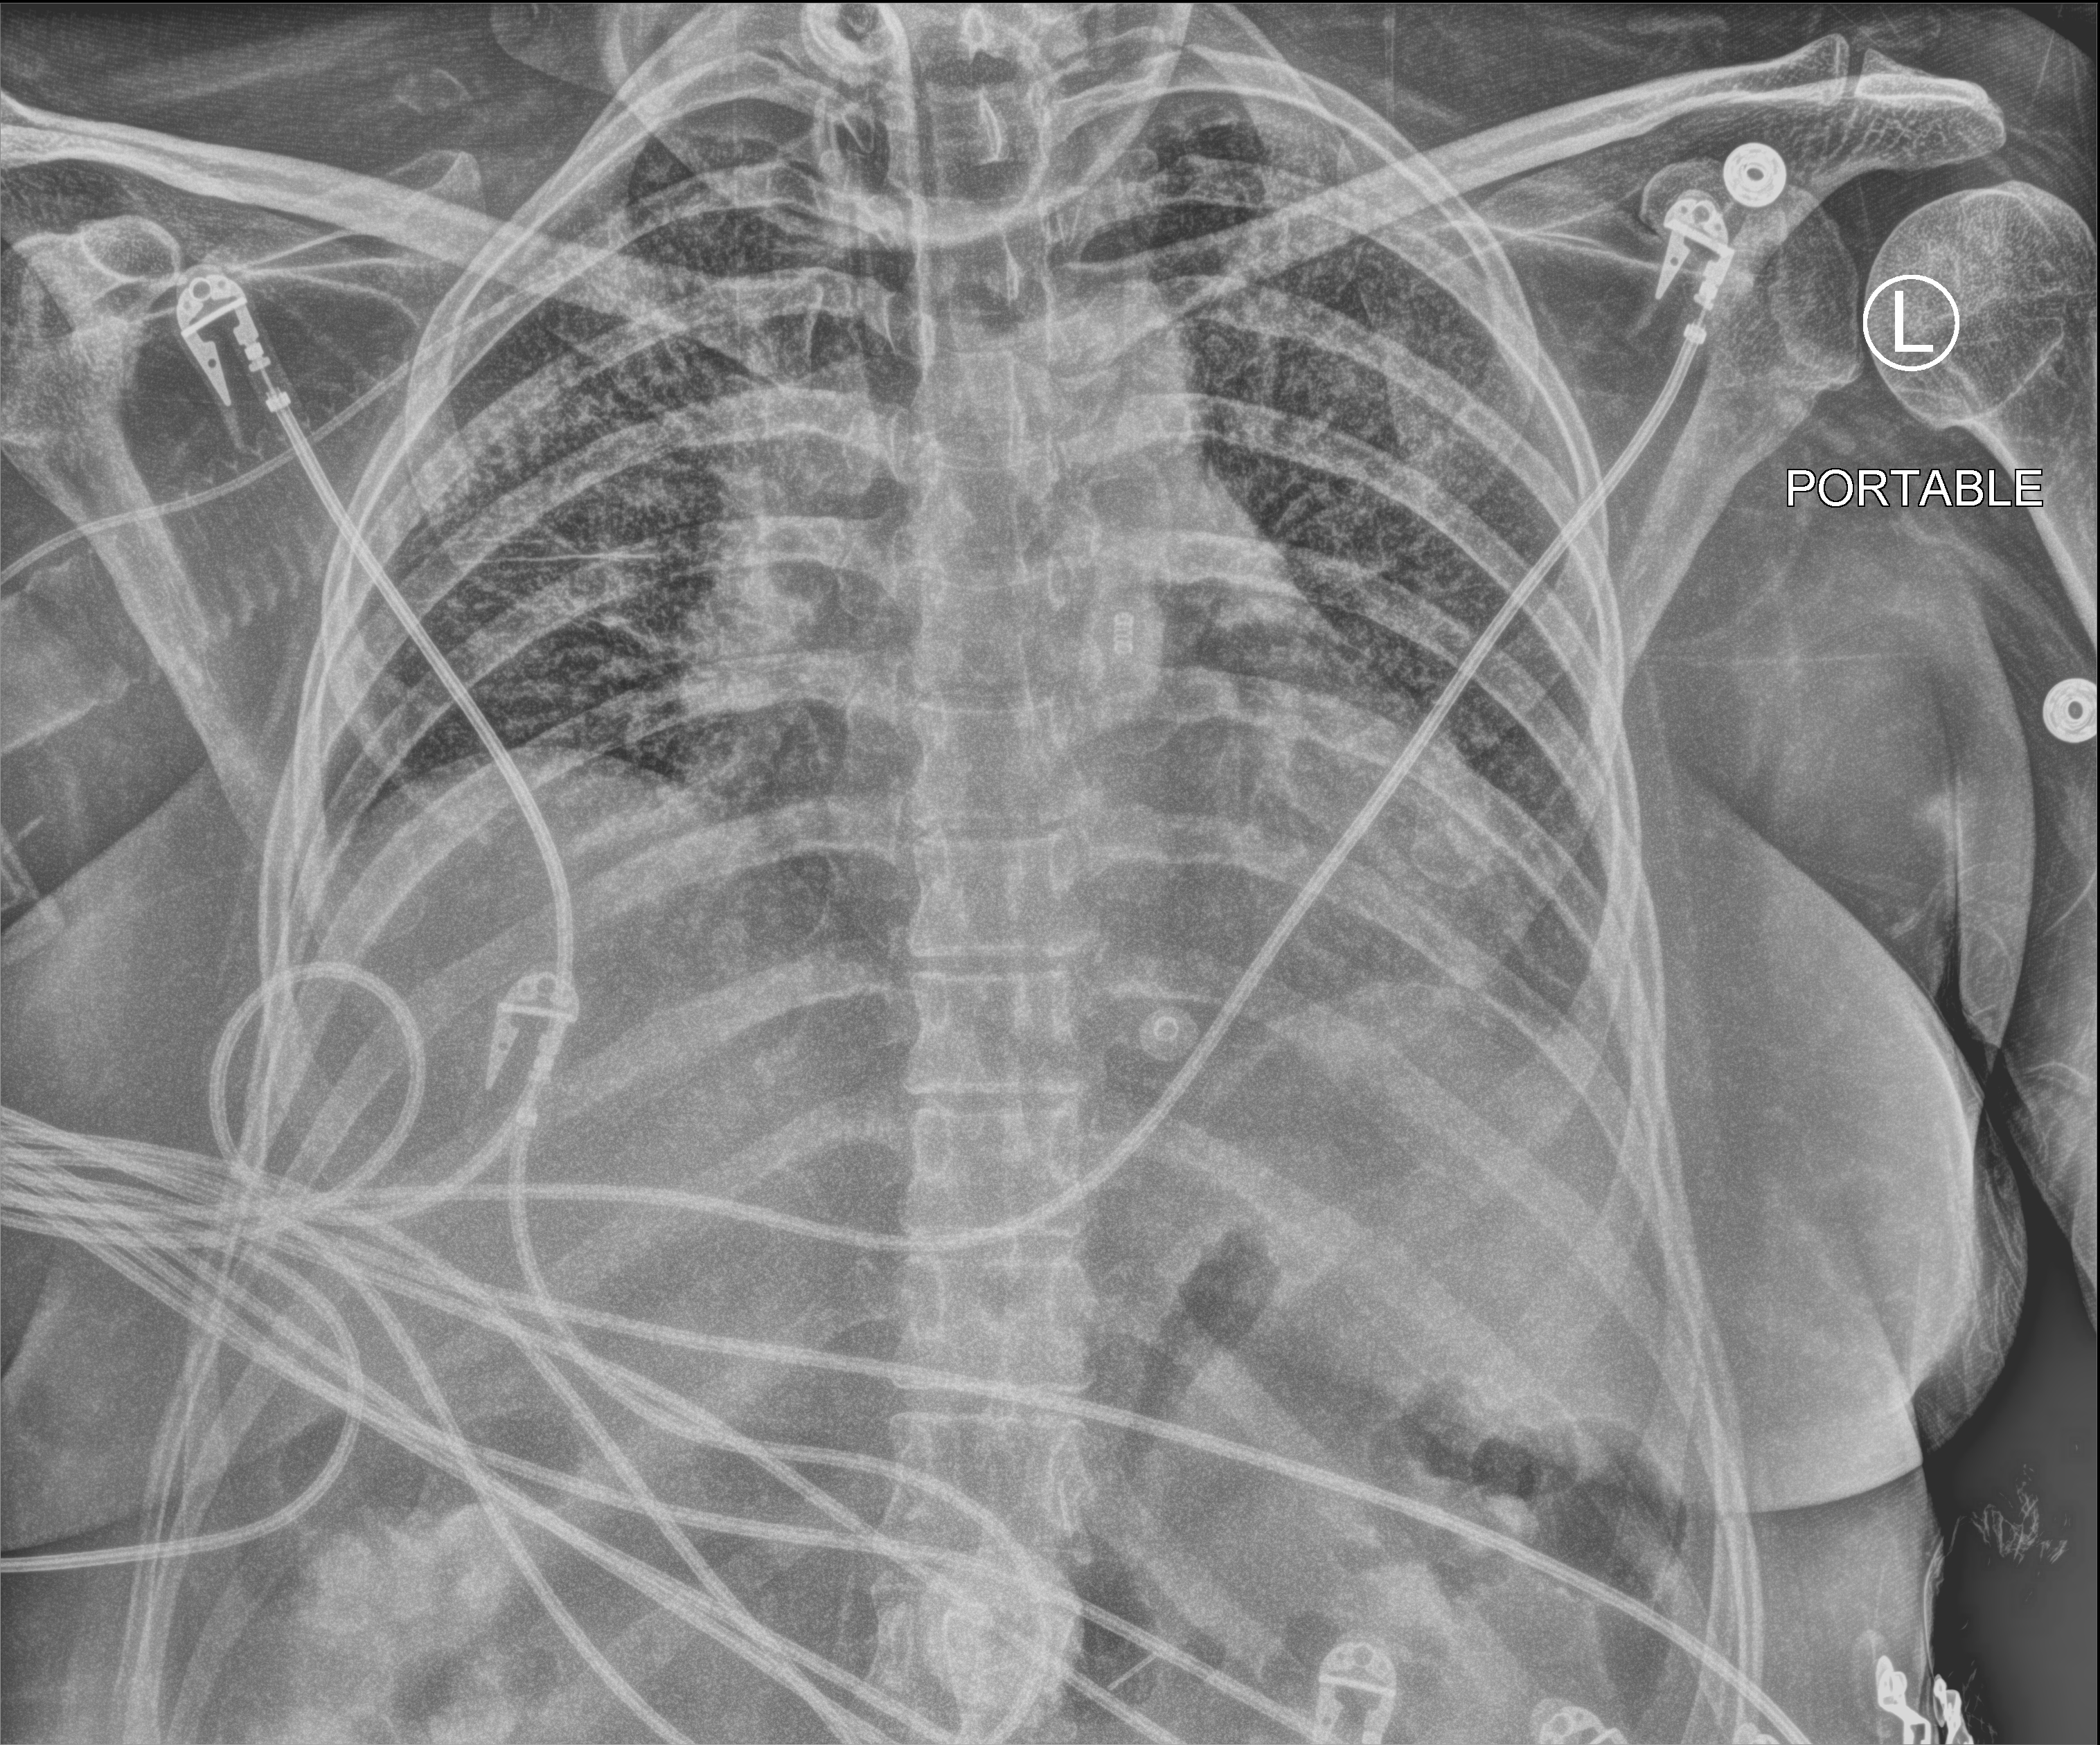
Chest X-ray (portable), anteroposterior (AP) projection. Female patient hospitalised with COVID-19, age 18–59 years.
From the hospital-stay record, not from the radiograph (when in the stay this image was taken is not recorded):
- chronic kidney disease (admission record): no